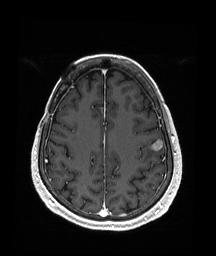
Brain MRI from a brain-tumour surgery series, one axial slice. Position 63 of 176 along the scan axis. T1-weighted post-contrast. 1 mm slice thickness. 216 × 256 image matrix, field of view 211 × 250 mm. From the clinical record (not read from this slice): histopathology: Metastatic Malignant Melanoma.
Outlined on this slice (manually delineated by an expert):
- tumour: bounding box [x1, y1, x2, y2] px = [151, 140, 163, 152]